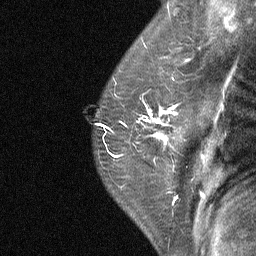
Breast MRI (dynamic contrast-enhanced), one sagittal slice. Position 49 of 64 along the scan axis. Dynamic contrast-enhanced study with each time point stored as its own series, time point 2 of 4 at this slice position (early post-contrast, ordered by acquisition time). 1.5 T. TE 4.8 ms, TR 27 ms. 2 mm slice thickness. 256 × 256 image matrix. Patient: female, 50 years. Case-level facts recorded for this patient, not image findings: setting: breast cancer imaged before/during neoadjuvant chemotherapy; receptor status: HER2-positive.
Annotated regions visible in this slice (semi-automatically segmented with operator editing):
- analysis volume of interest (the breast-tissue region the enhancement analysis was run in; not a lesion): box from (x=123, y=91) to (x=189, y=177) px
- tumour enhancement mask (voxels above the 90 % enhancement threshold inside the analysis volume of interest): (x=149, y=107)–(x=176, y=142)